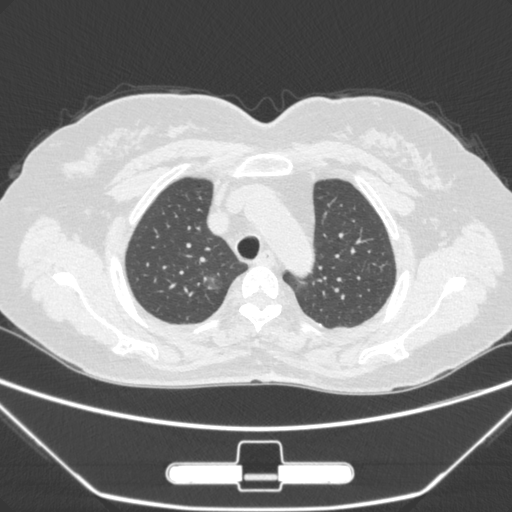
Chest CT, one axial slice. Slice 224 of 275 in the series (ordered by position). 120 kVp. Lung window (W 1500 / L -600 HU). 512 × 512 image matrix. Patient: female, 63 years. Case-level facts recorded for this patient, not image findings: clinical TNM (as recorded): T1a N0 M0.
Annotated regions visible in this slice (bounding box drawn by a radiologist):
- lung tumour (recorded histology: adenocarcinoma): bounding box [x1, y1, x2, y2] px = [195, 270, 231, 302]